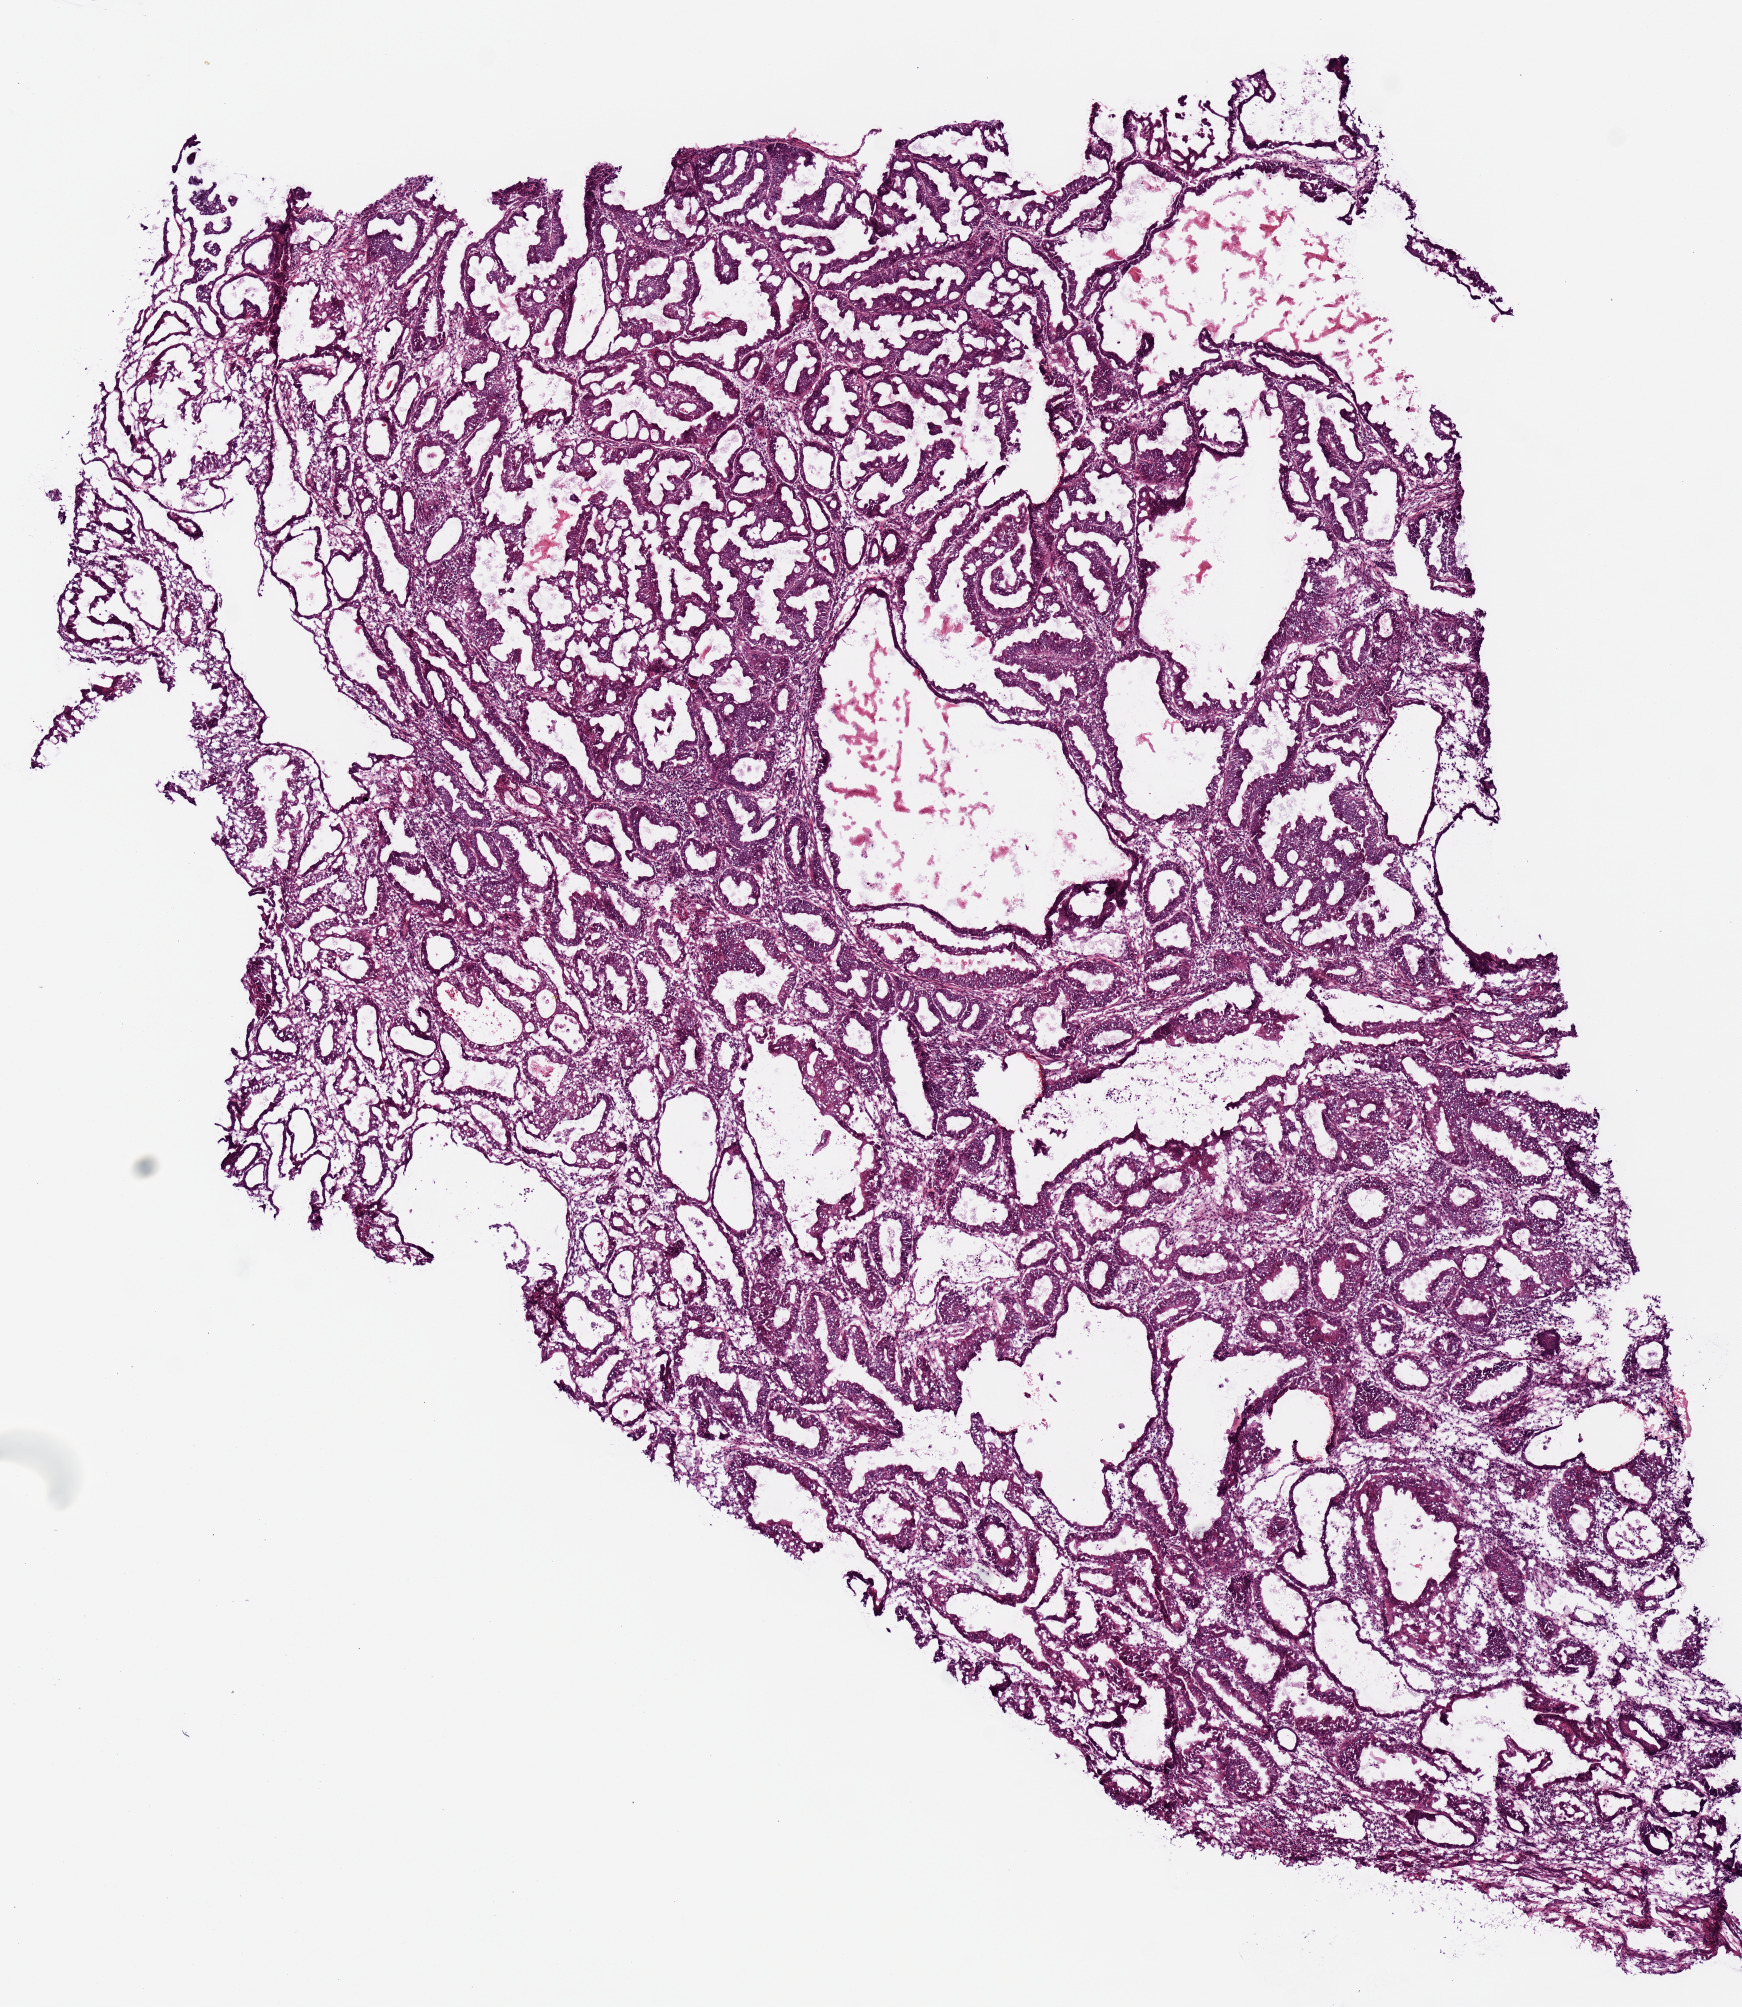
Hematoxylin and eosin (H&E) stained whole-slide image, a low-resolution overview of the entire scanned area, about 6.9 x 7.9 mm (slide scanned at 20x), frozen section from the top of the tissue portion, sample: primary tumour, uterus. Female patient; age at initial diagnosis 52 years. Histologic grade: G3 (poorly differentiated). Slide review estimates, as recorded: tumour cells 70%, tumour nuclei 60%, normal cells 0%, stromal cells 15%, necrosis 15%. Infiltration values recorded for this section: lymphocyte infiltration 0%, monocyte infiltration 0%, neutrophil infiltration 0%.
Pathologic diagnosis: Endometrioid adenocarcinoma, NOS. FIGO stage: IIB.